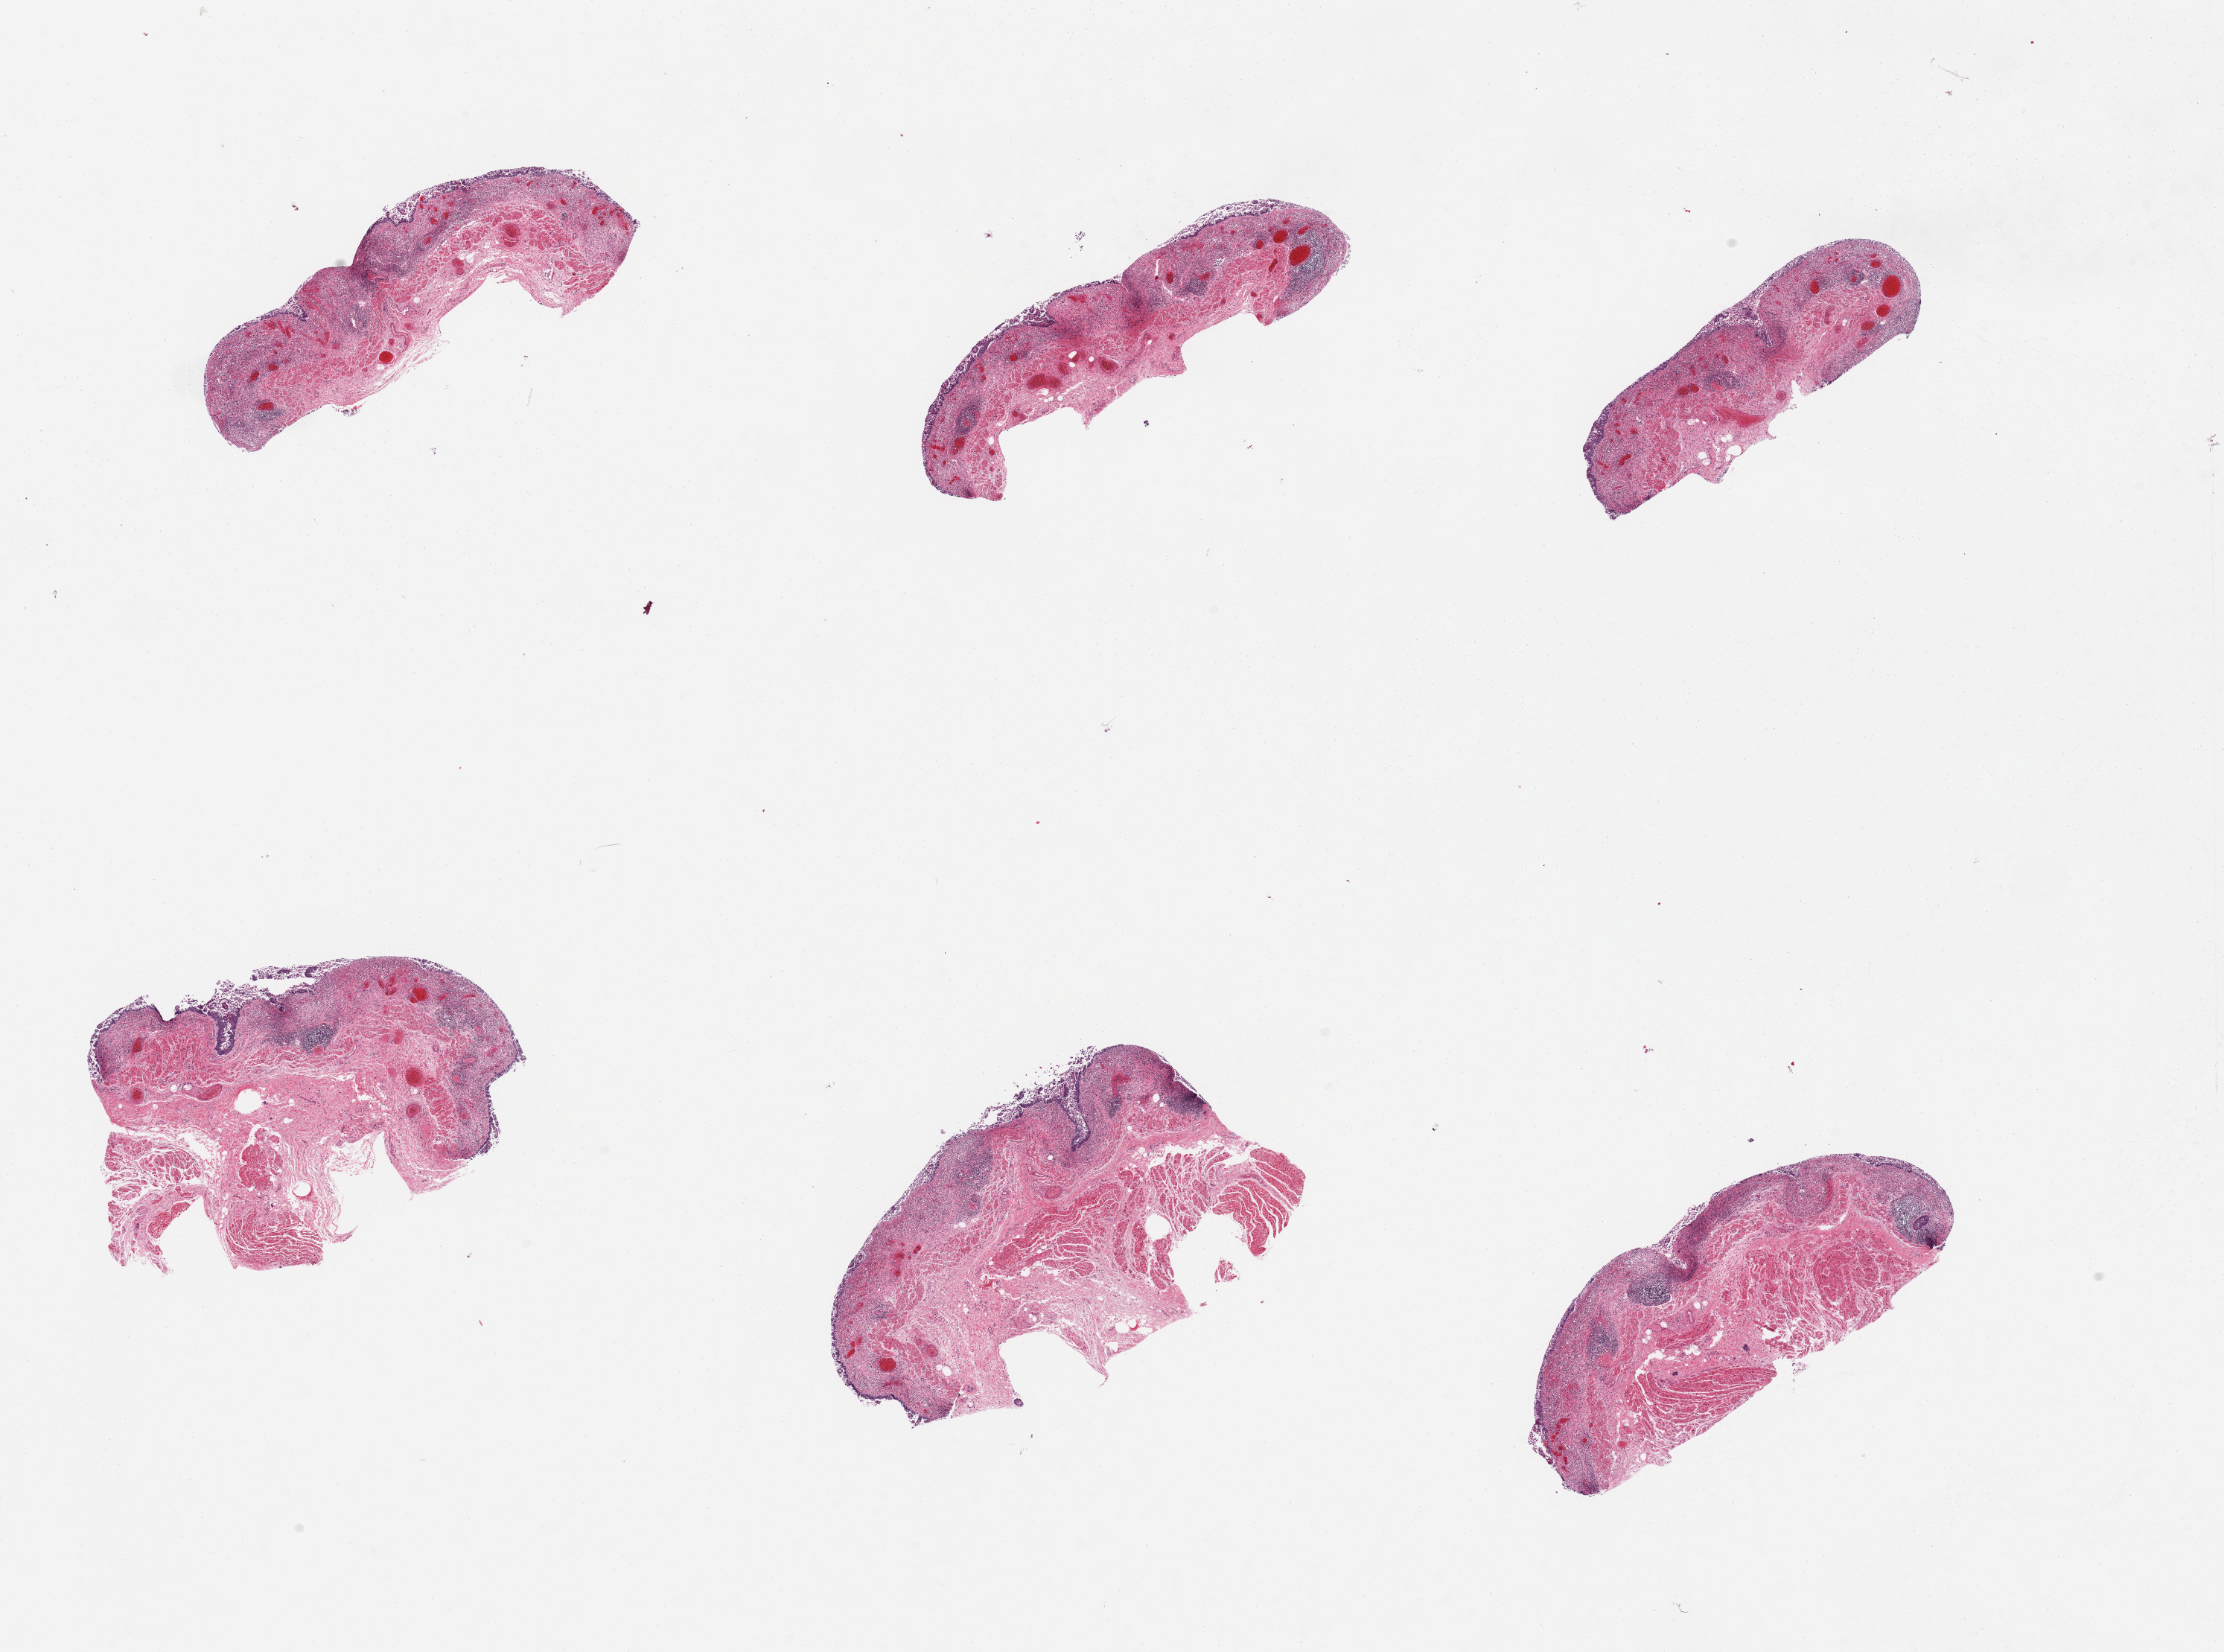
Digitized haematoxylin and eosin-stained section, a low-resolution overview of the entire scanned area, about 23.6 x 17.6 mm; PAXgene-fixed paraffin-embedded (PFPE) section; section of esophageal mucous membrane (target tissue); tissue donor sample. Donor sex: male.
• pathologist's review note for this sample: 6 pieces, acute and chronic esophagitis with erosion, includes muscularis